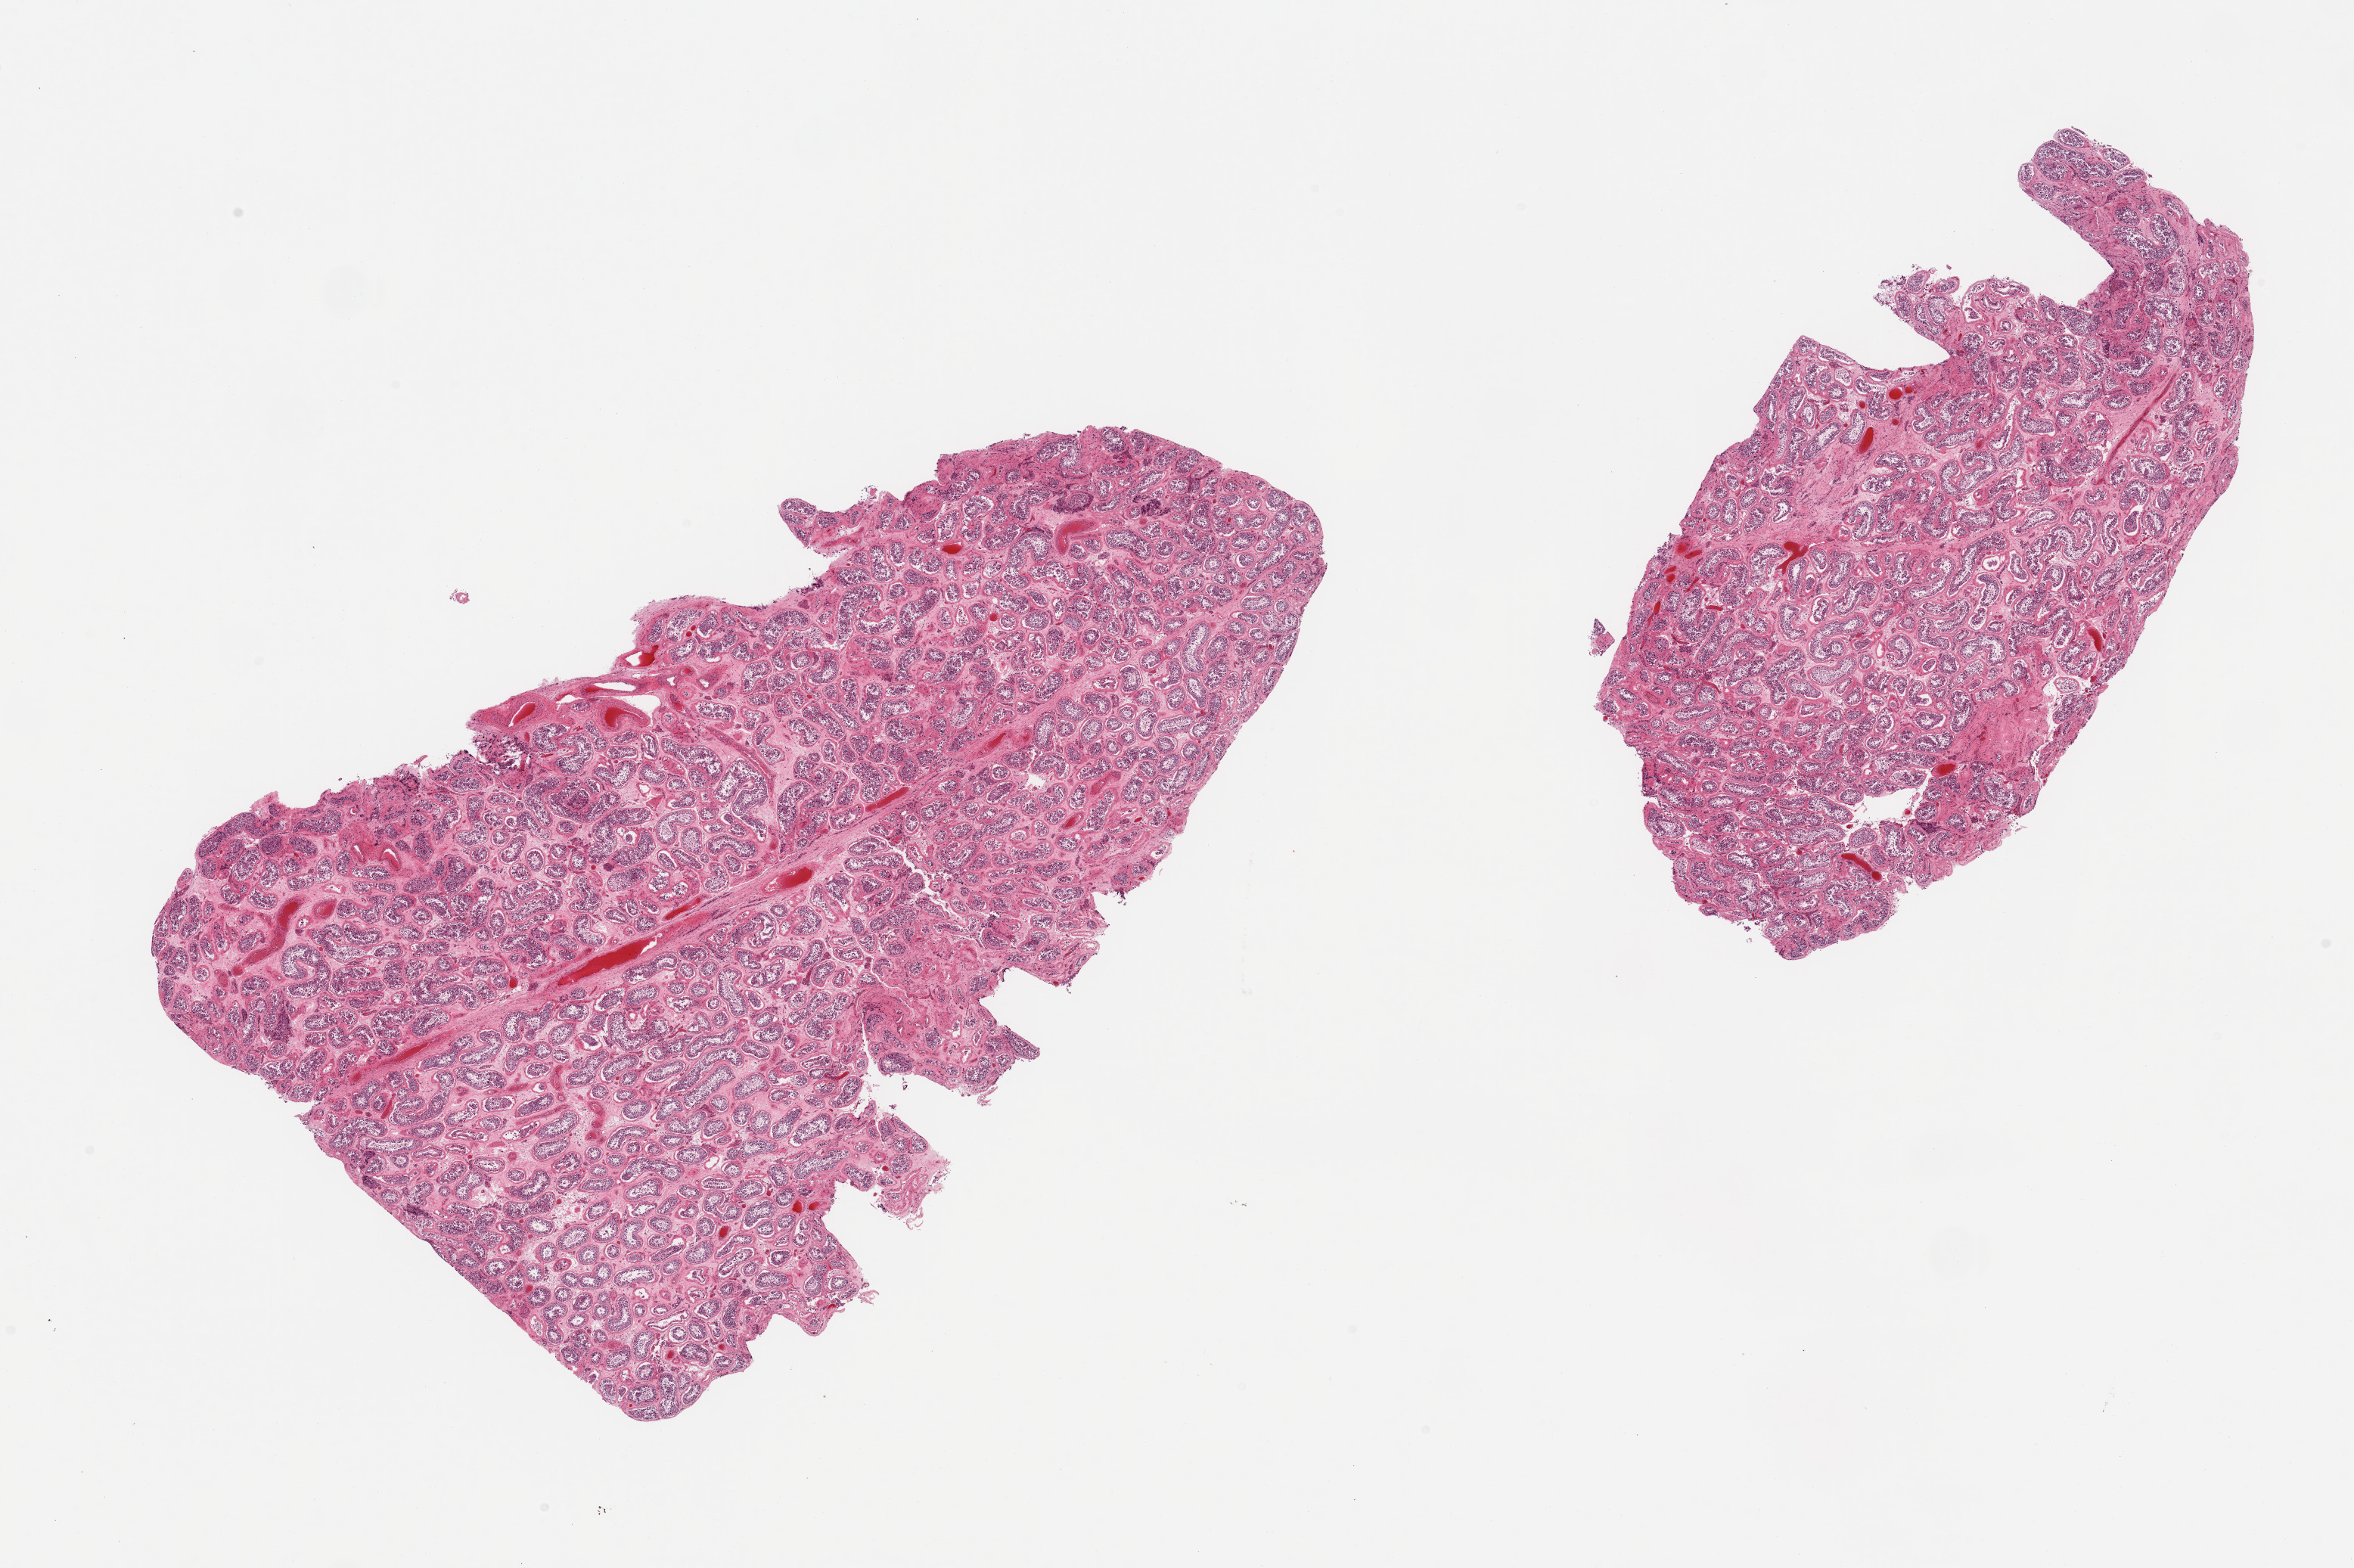
Whole-slide image, haematoxylin and eosin stain — a low-resolution overview of the entire scanned area, about 24.6 x 16.4 mm (slide scanned at 20x). PAXgene-fixed paraffin-embedded (PFPE) section. Section of testis (target tissue). Tissue donor sample. Donor sex: male.
Review note (as recorded): 2 pieces, spermatogenesis appears reduced. Interstitial fibrosis, foci of tubular hyalinization noted.